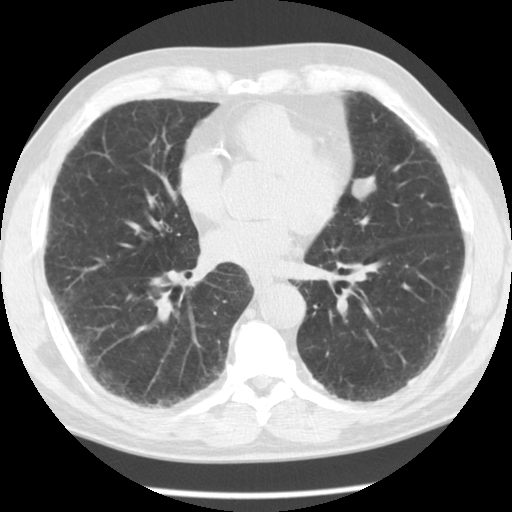
Low-dose screening chest CT, one axial slice. Position 51 of 113 along the scan axis. Reconstruction kernel STANDARD. 120 kVp. Lung window (W 1500 / L -600 HU). 2.5 mm slice thickness. 512 × 512 image matrix, field of view 330 × 330 mm.
Outlined on this slice (outlined manually by an expert reader):
- lesion 1 (nodule, upper lobe of left lung): box from (x=352, y=179) to (x=376, y=201) px